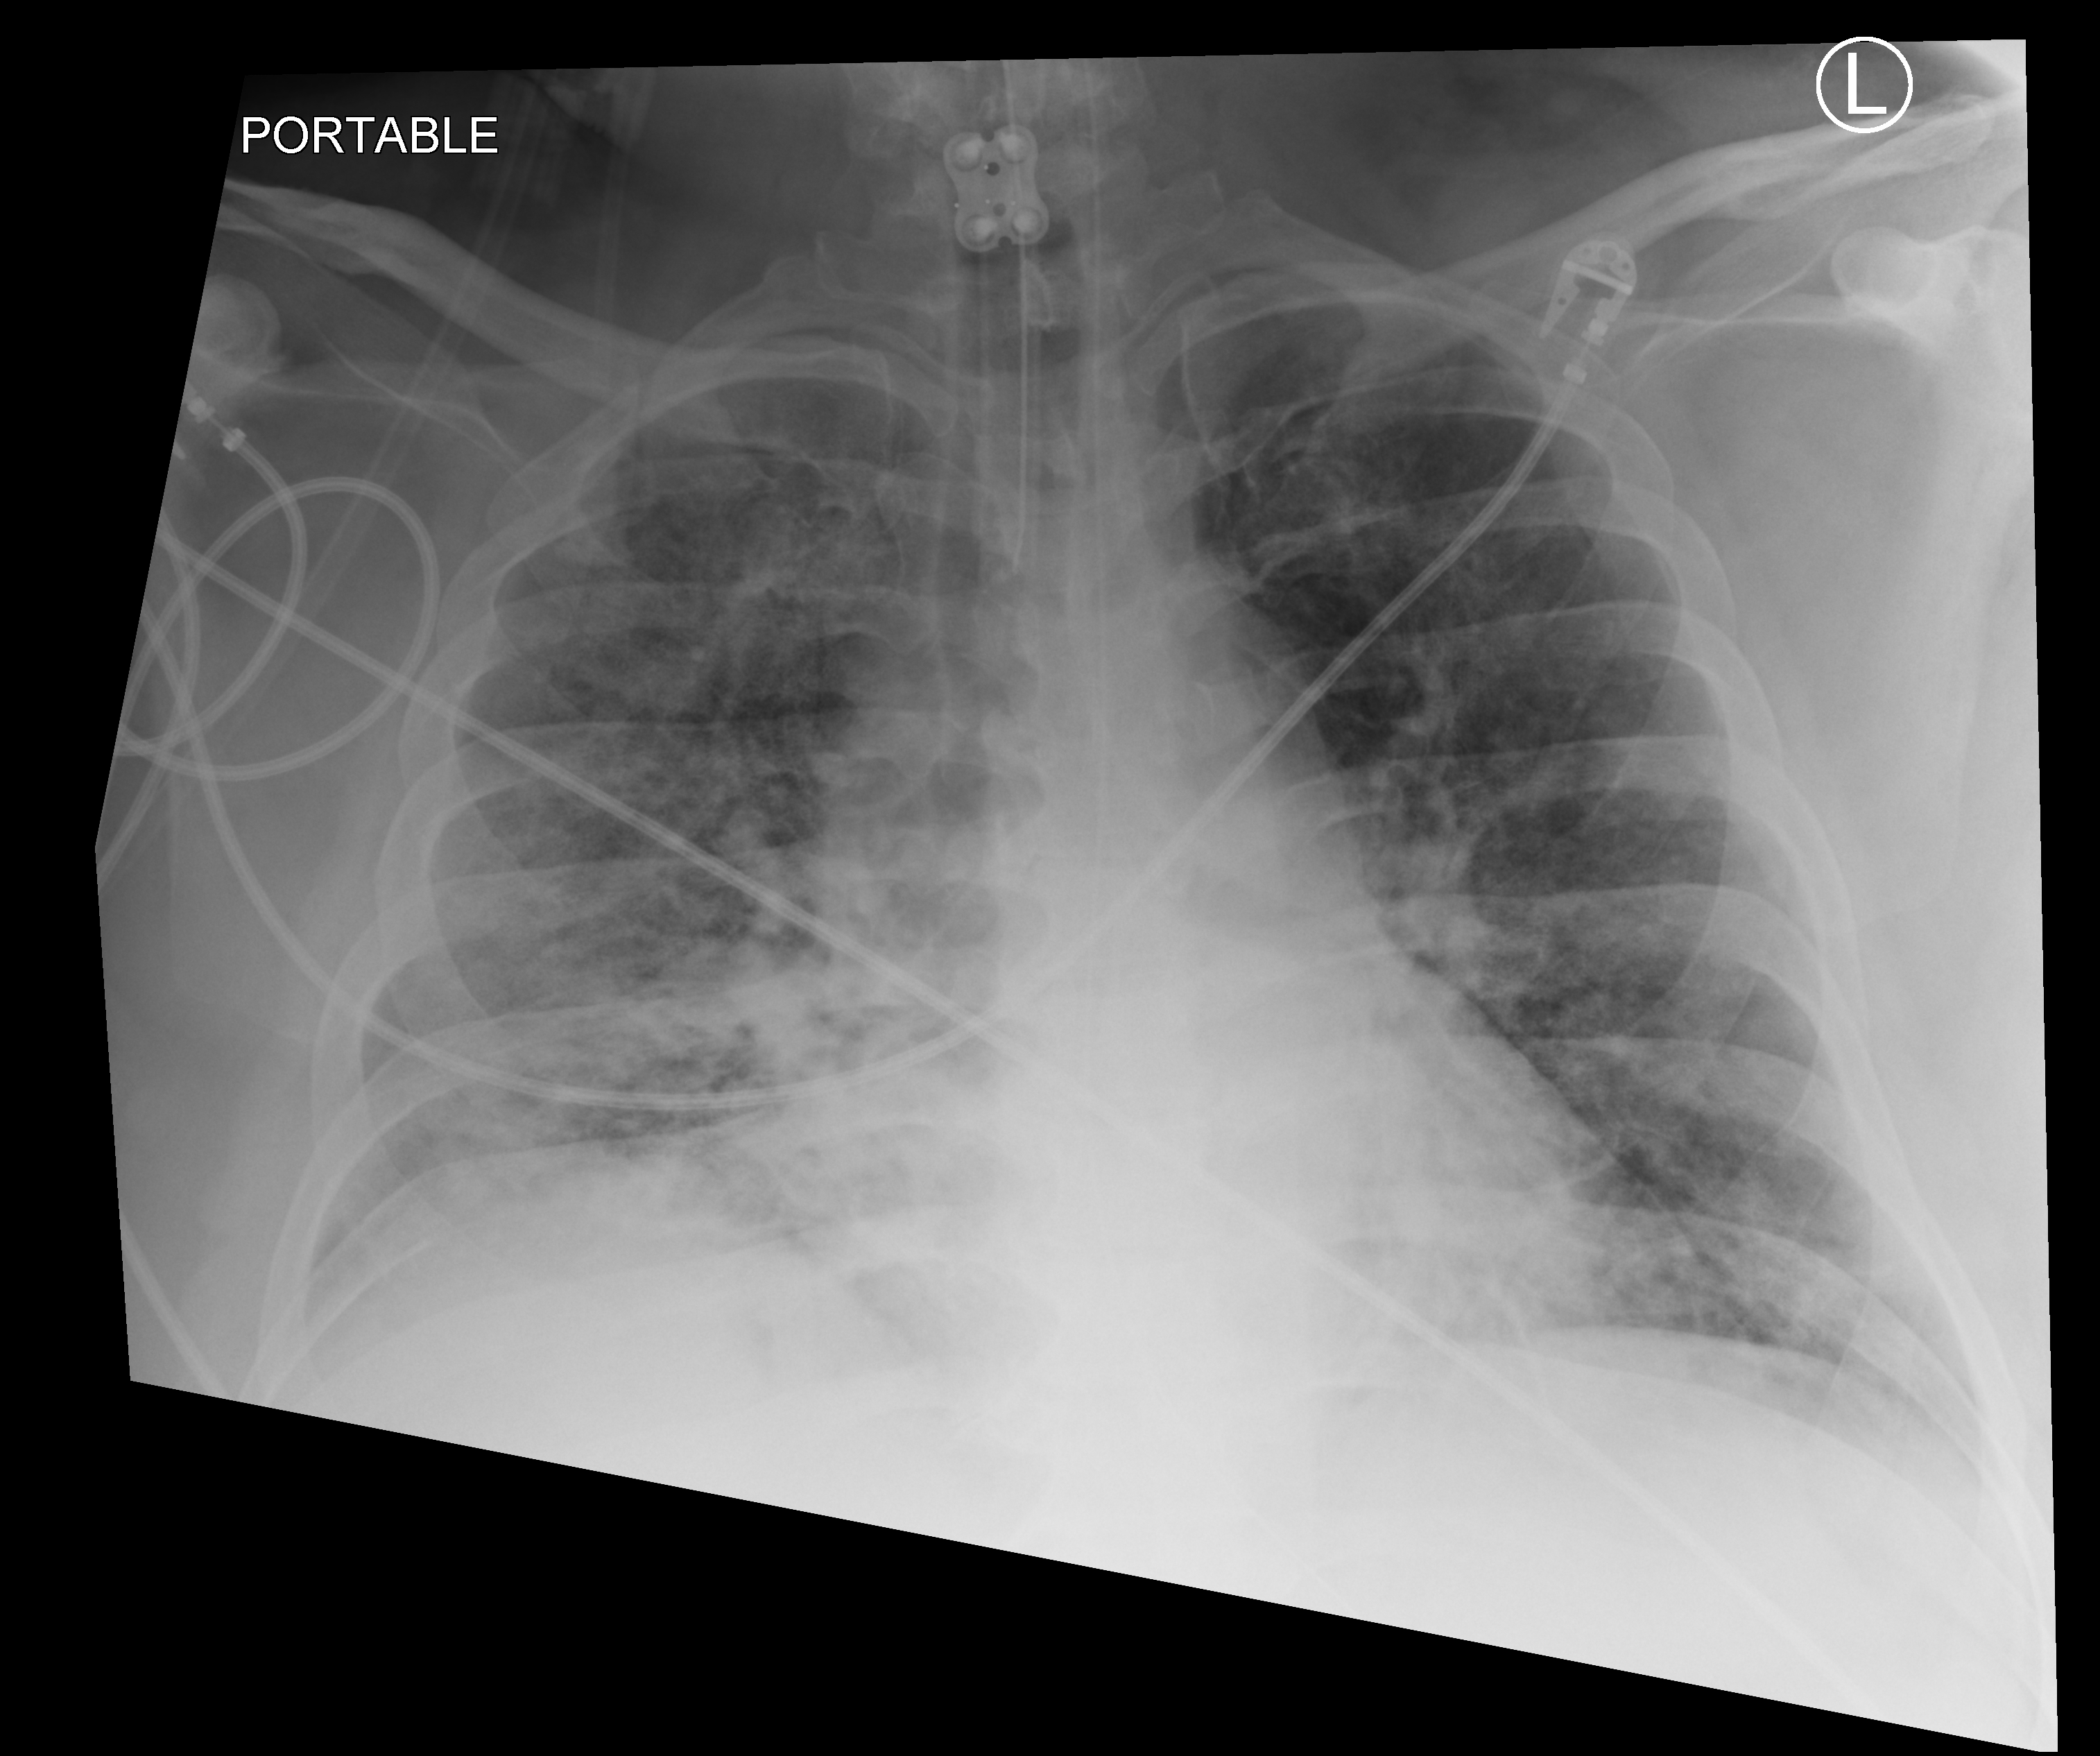
Chest X-ray (portable); anteroposterior (AP) projection. Male patient hospitalised with COVID-19, age 18–59 years.
Admission-level facts for this patient (not findings on this image; timing relative to this image not recorded):
- smoking status (admission record): never